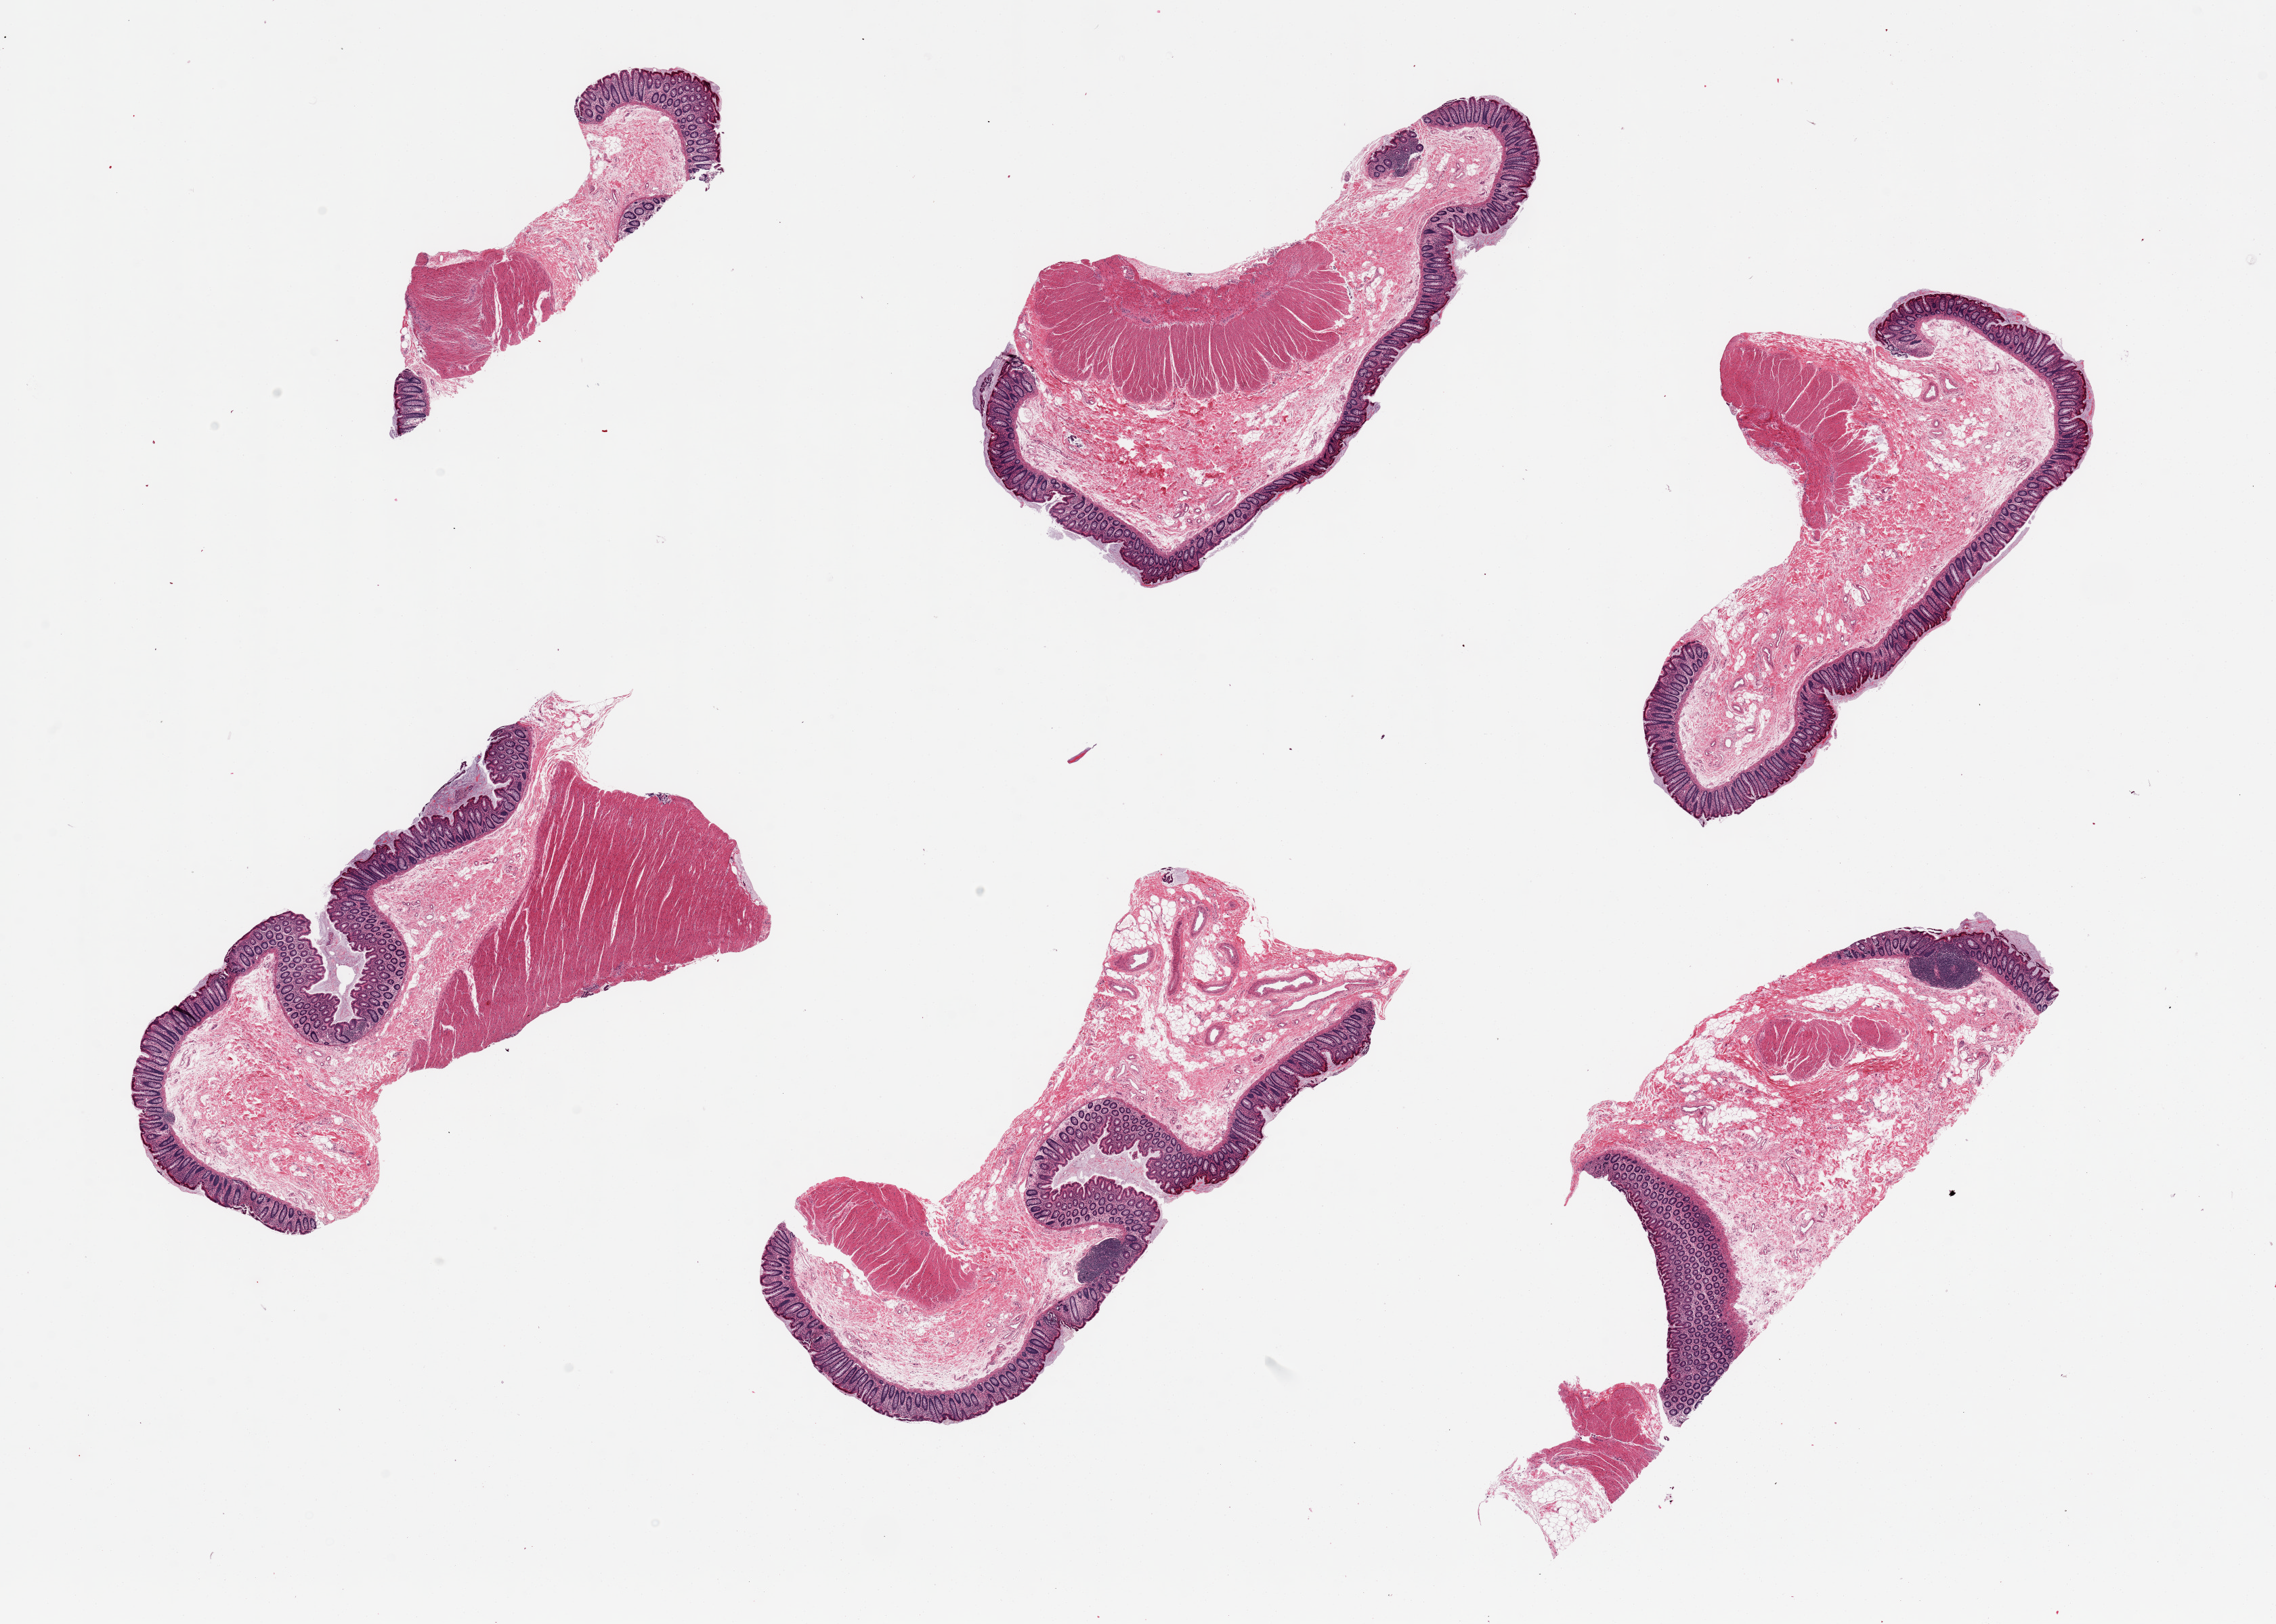
Hematoxylin and eosin (H&E) whole-slide image, brightfield, a low-resolution overview of the entire scanned area, about 26.6 x 19.0 mm (slide scanned at 20x). PAXgene-fixed, paraffin-embedded tissue. Sampled site (target tissue): sigmoid colon. Tissue donor sample. Donor sex: female.
Reviewer comment on this tissue sample: 6 pieces, all with both muscularis and mucosa.